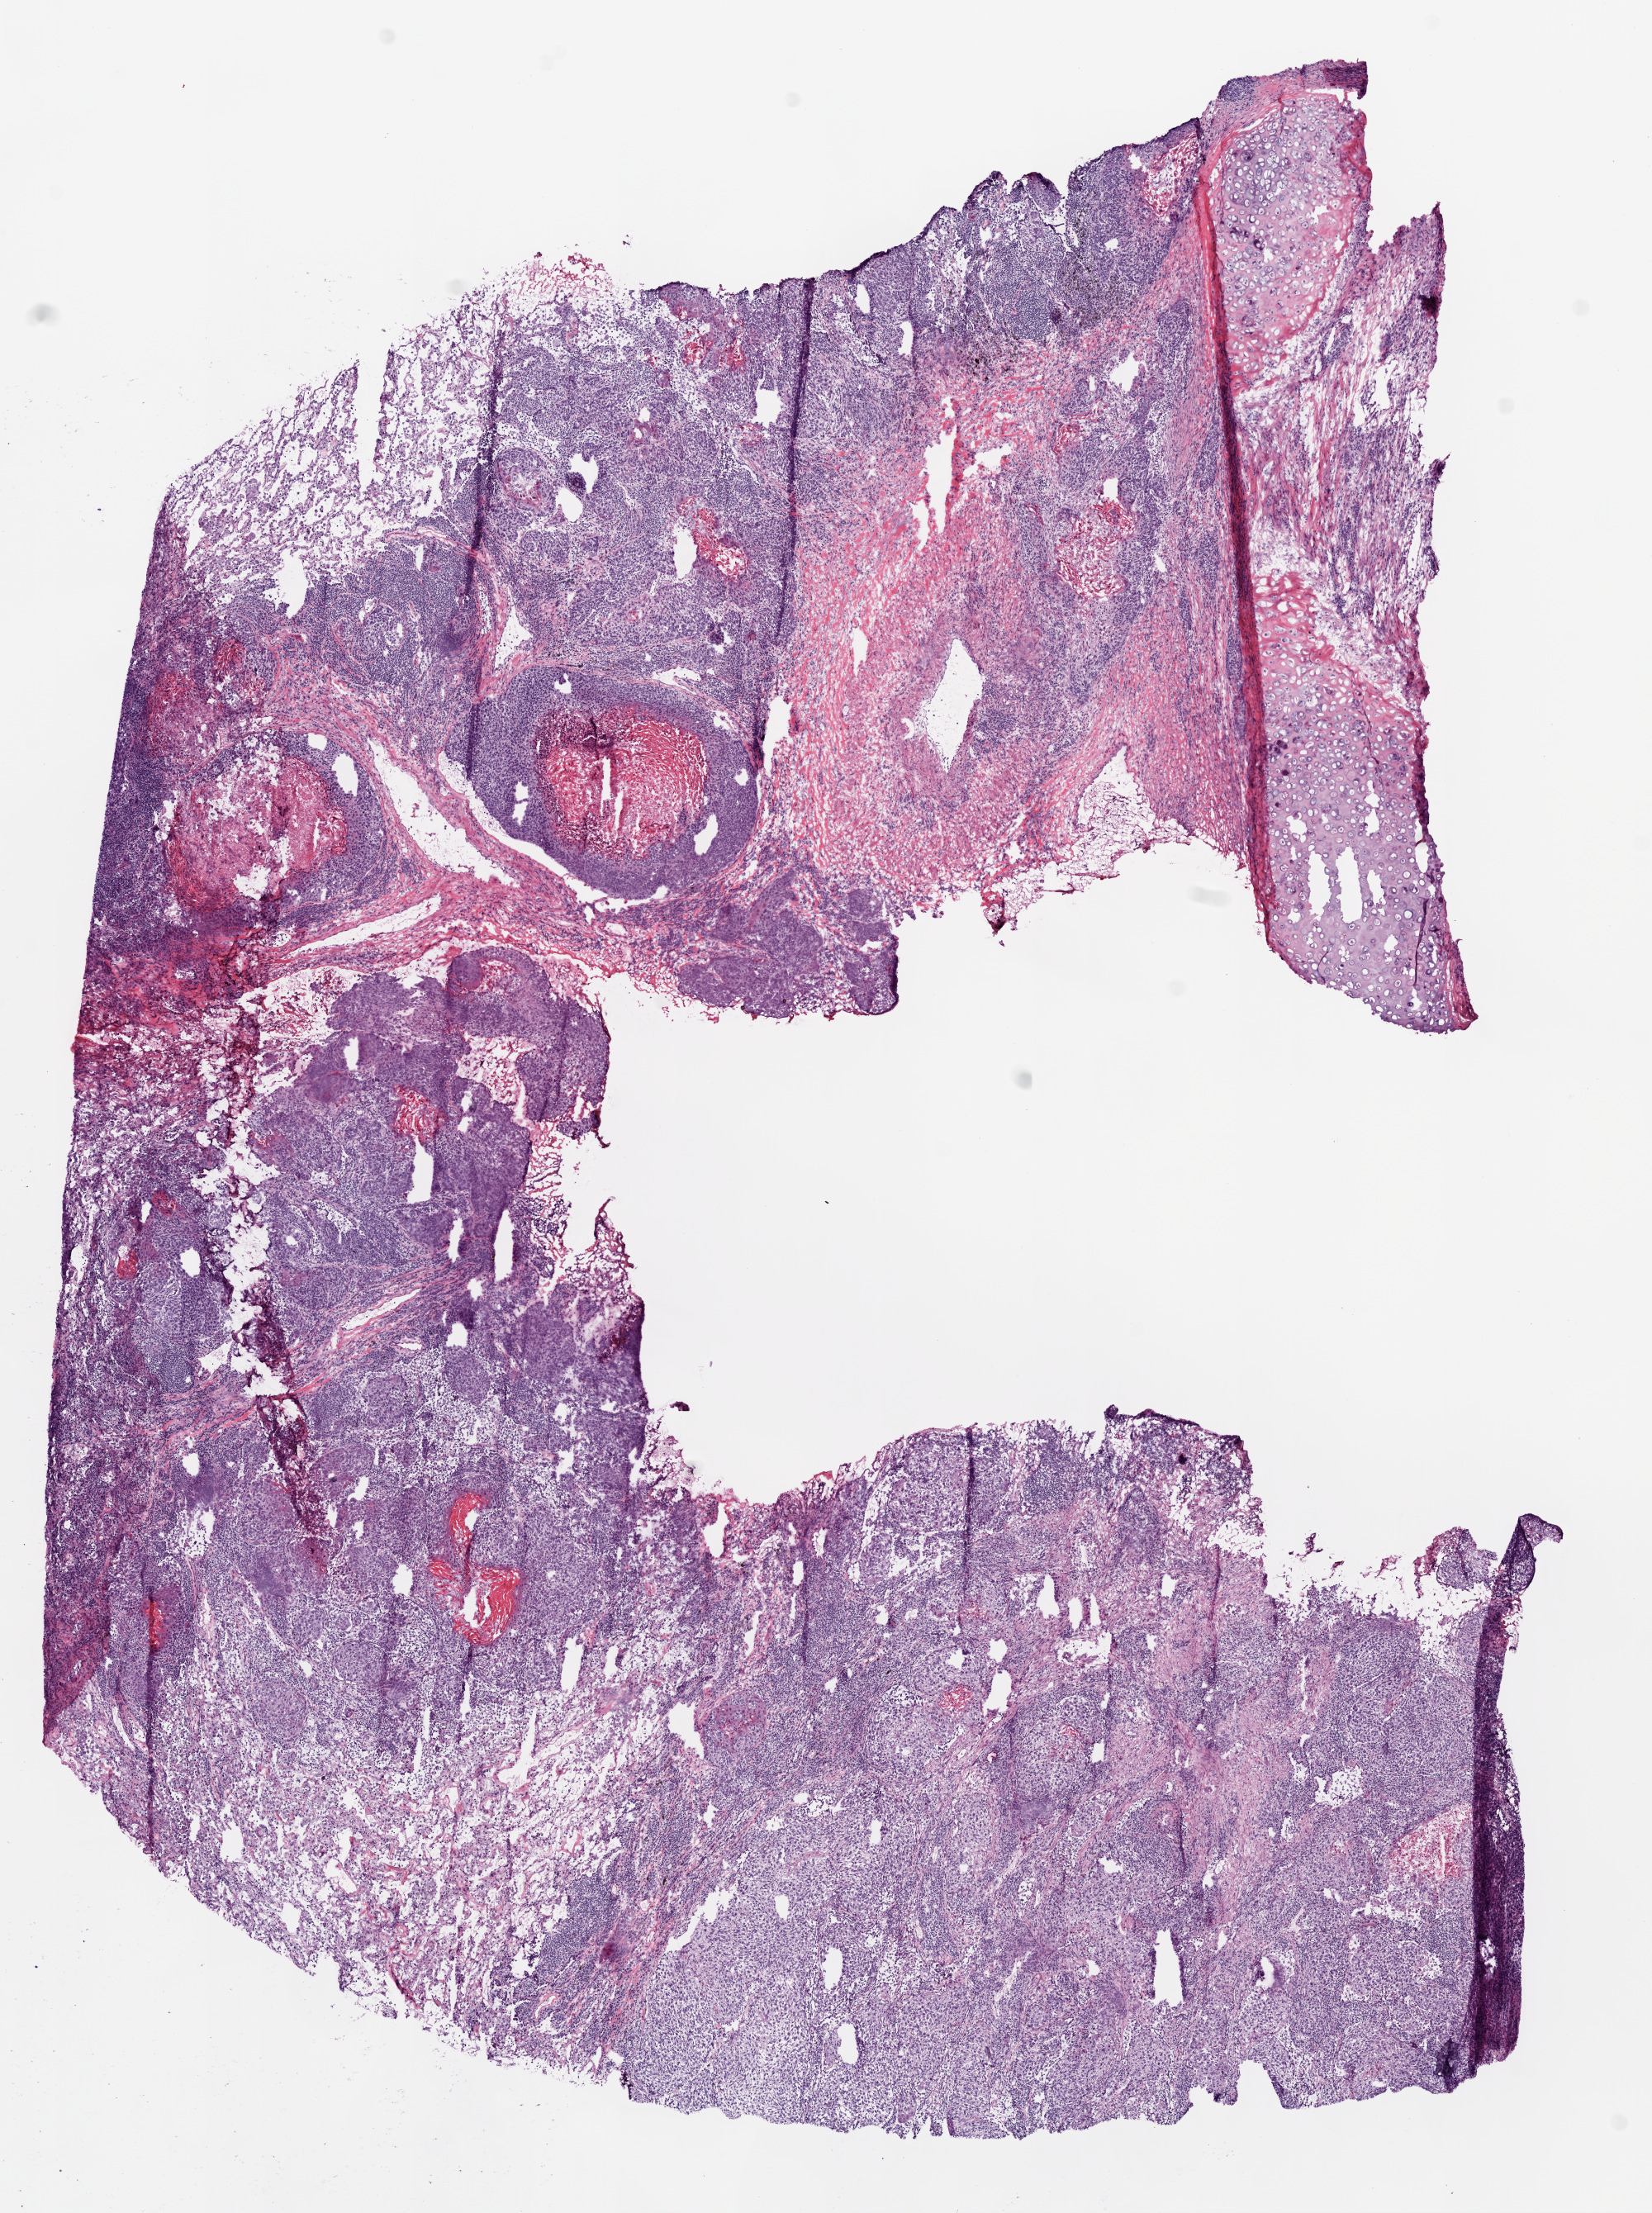
Digitized H&E-stained tissue section (whole slide) — whole scanned area (about 8.0 x 10.7 mm, slide scanned at 20x) shown as a low-resolution overview, frozen section from the top of the tissue portion, primary tumour sample from the lung. Male, age 62 years at initial diagnosis. Pathologist review of this section (percent, as recorded): tumour cells 65%, tumour nuclei 70%, normal cells 10%, stromal cells 10%, necrosis 15%.
Laterality: right. Pathologic diagnosis: Squamous cell carcinoma, NOS (lower lobe, lung). AJCC pathologic stage: IIIB (6th edition).